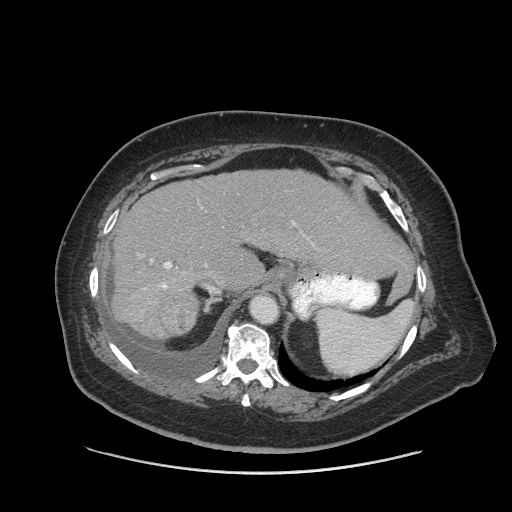
Contrast-enhanced abdominal CT (liver protocol), one axial slice. Position 61 of 91 along the scan axis. Reconstruction kernel STANDARD. 140 kVp. Soft-tissue window (W 400 / L 40 HU). 2.5 mm slice thickness. 512 × 512 image matrix, field of view 420 × 420 mm. From the clinical record (not read from this slice): diagnosis: hepatocellular carcinoma (patient treated with transarterial chemoembolisation; whether this scan precedes or follows treatment is not stated here); TNM stage (as recorded): Stage-I; Child-Pugh class: A.
Structures marked on this image (semi-automatic segmentation, software-assisted and operator-edited):
- liver parenchyma outside the tumour (the mass and vessels are separate outlines, so this box may not span the whole liver): box from (x=112, y=170) to (x=400, y=338) px
- mass: (x=159, y=288)–(x=198, y=338)
- liver vessels: (x=151, y=223)–(x=294, y=288)